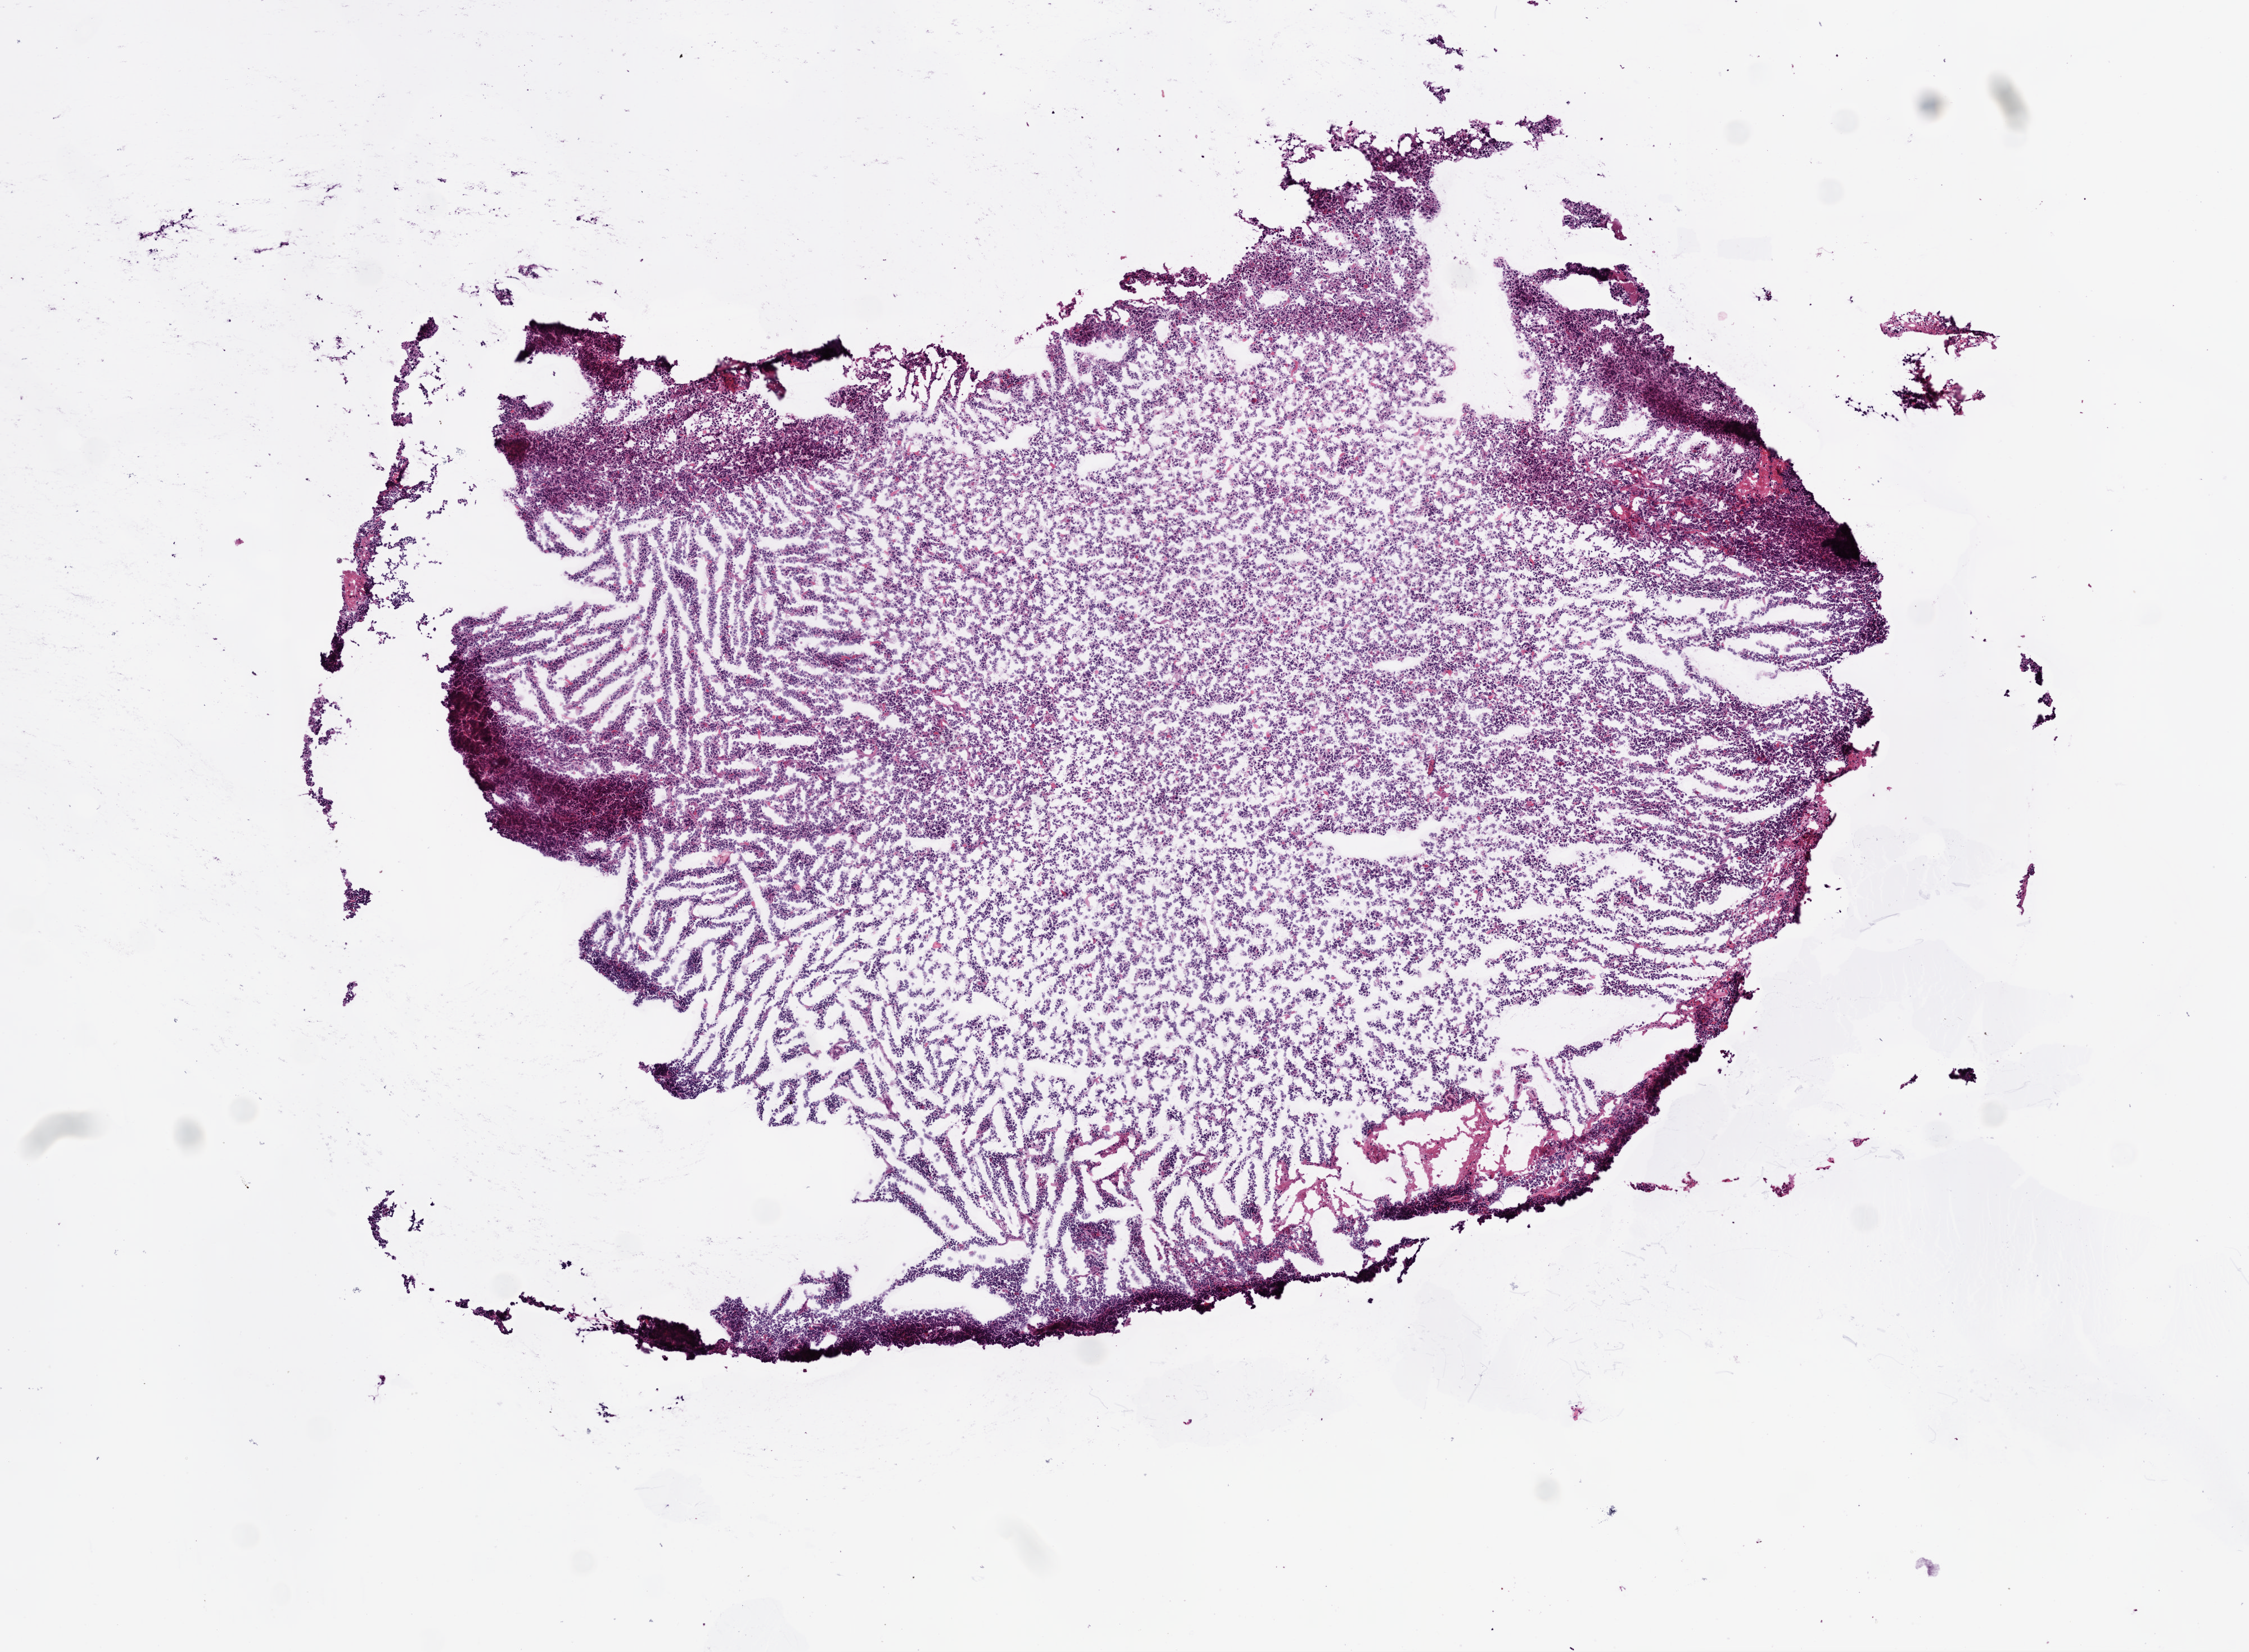
Whole-slide histology image, H&E-stained — shown as a low-resolution overview of the whole scanned area (about 8.0 x 5.9 mm); frozen section from the bottom of the tissue portion; primary tumour sample from the brain. Patient: male, age at initial diagnosis 40 years. Pathologist review of this section (percent, as recorded): tumour cells 100%, tumour nuclei 85%, normal cells 0%, stromal cells 0%, necrosis 0%.
Diagnosis: Glioblastoma.